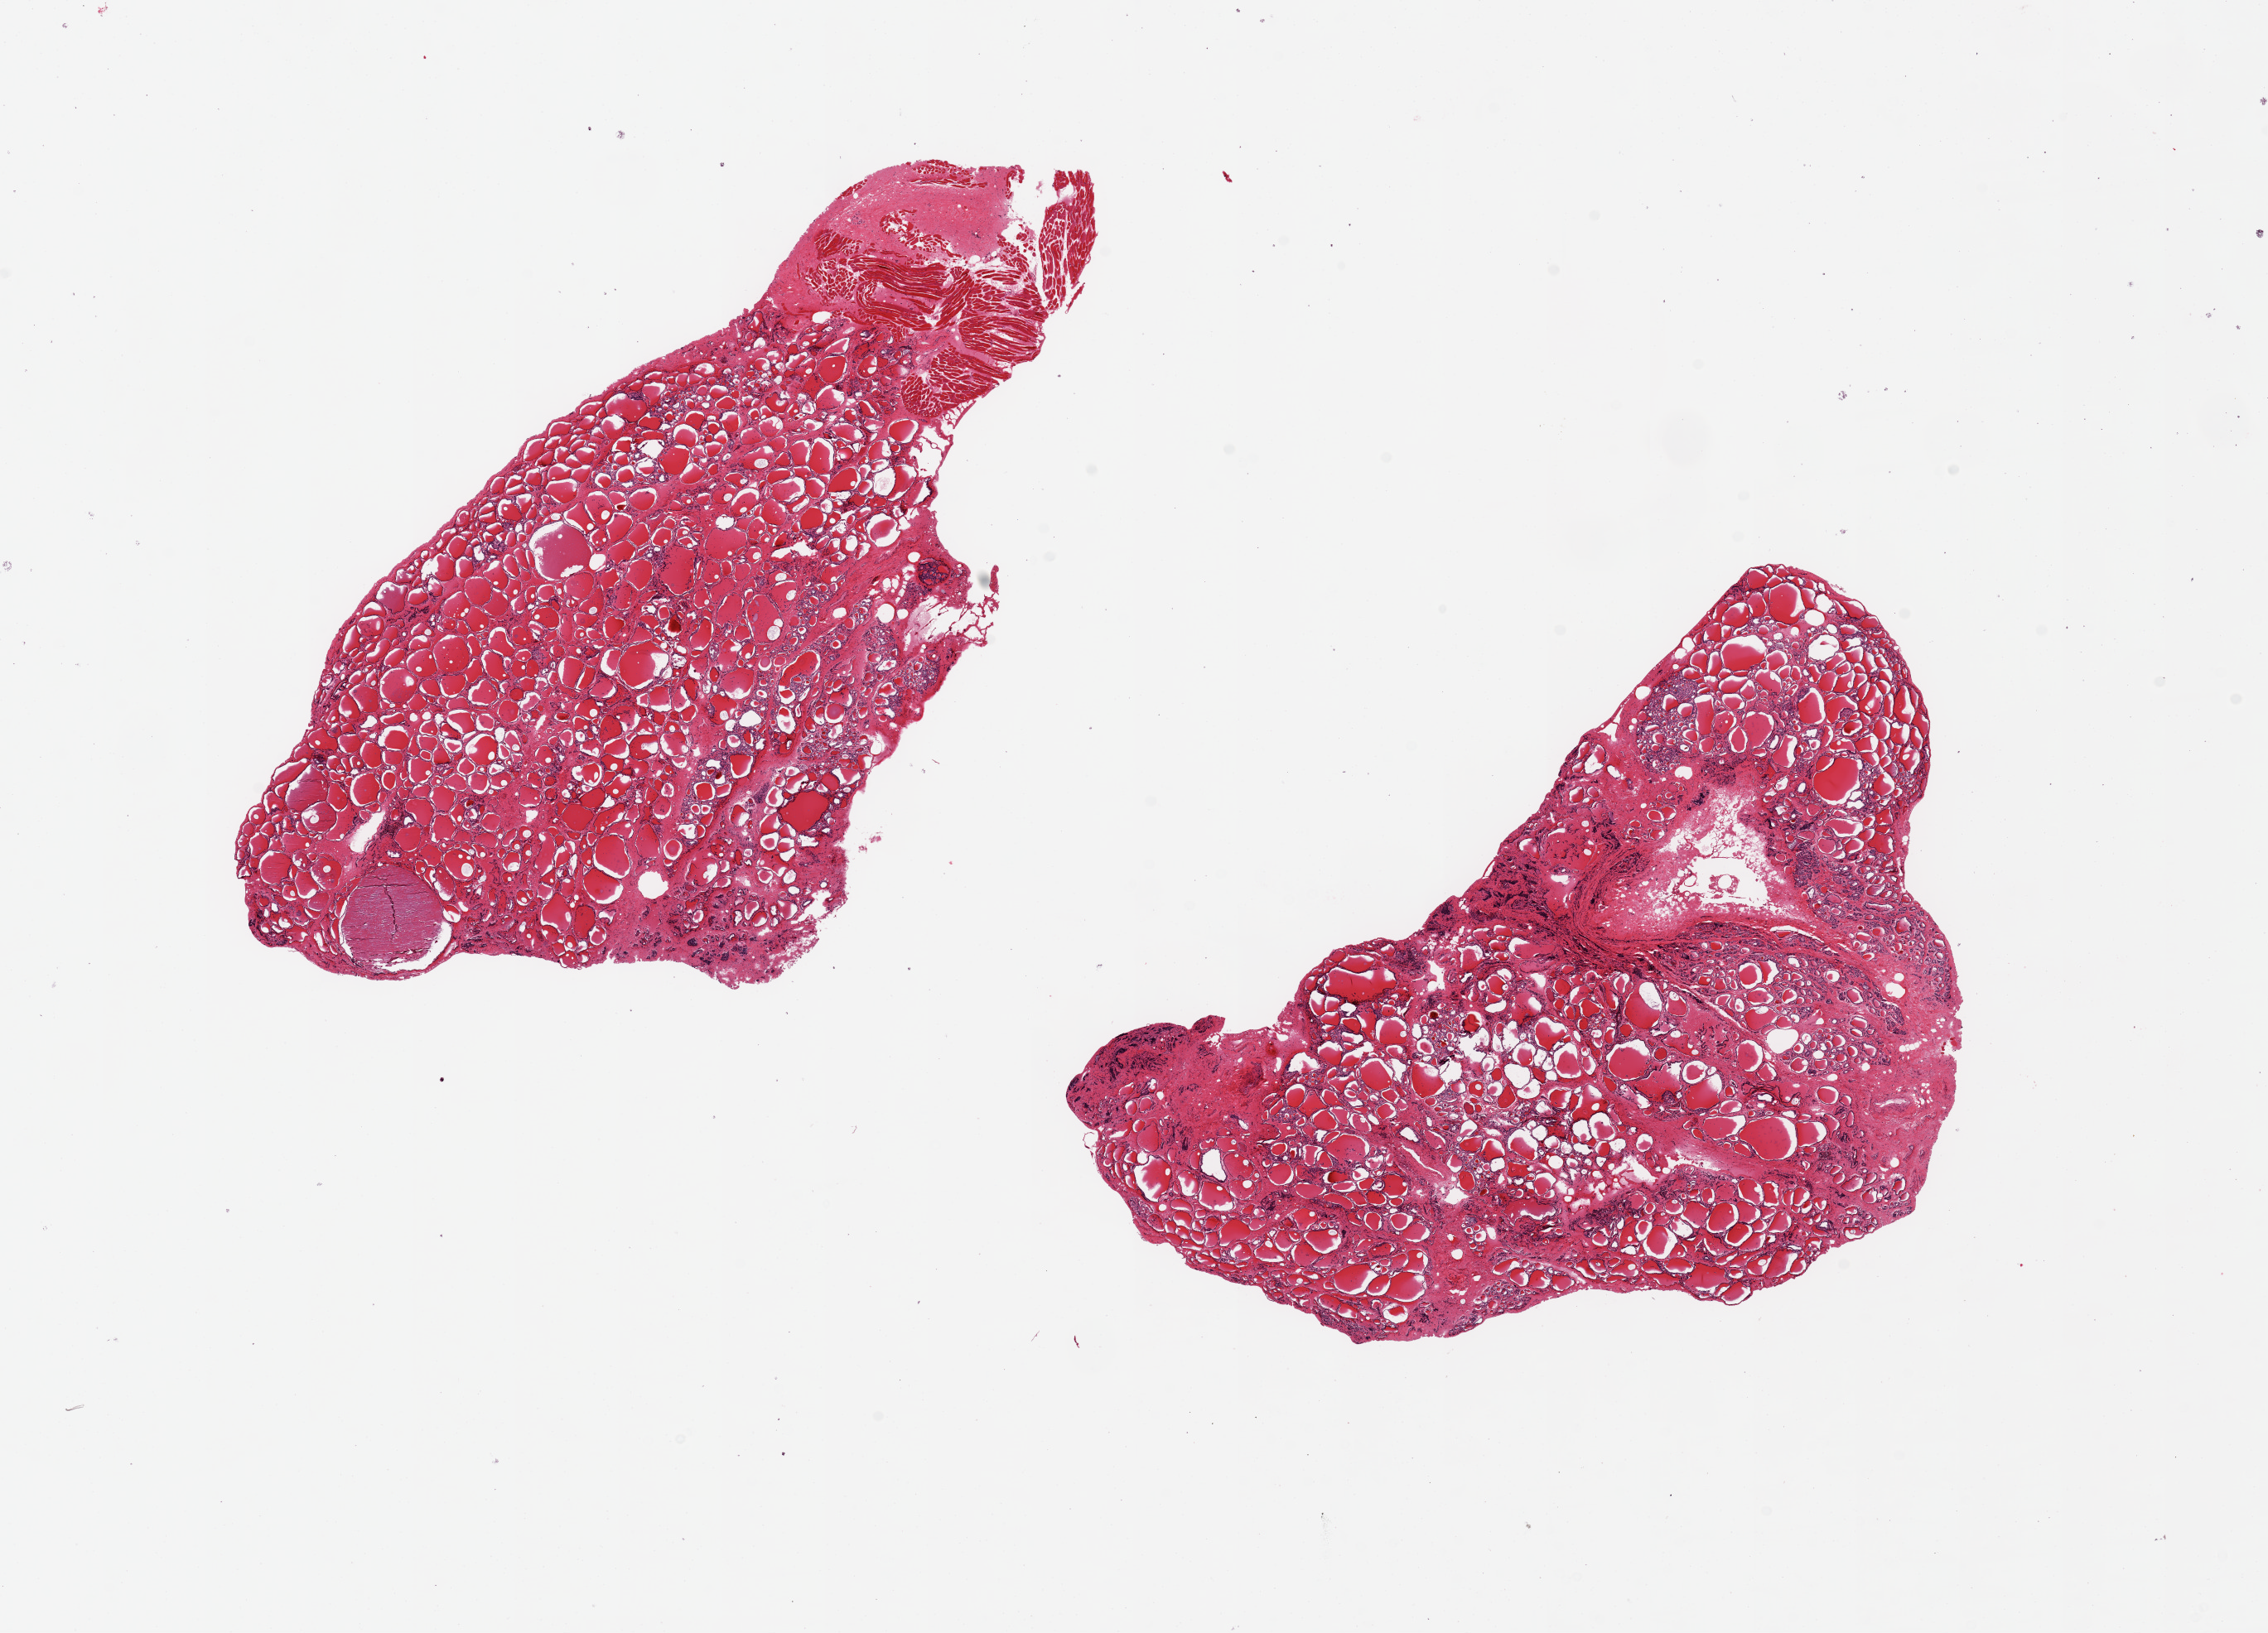
Whole-slide image, haematoxylin and eosin stain — shown as a low-resolution overview of the whole scanned area (about 21.7 x 15.6 mm, from a 20x scan), PAXgene-fixed, paraffin-embedded tissue, target tissue: thyroid, donor tissue sample. Donor: male.
Pathologist's review note for this sample: 2 ~9.5x5.5mm aliquots. Adenomatoid nodules with regressive changes.